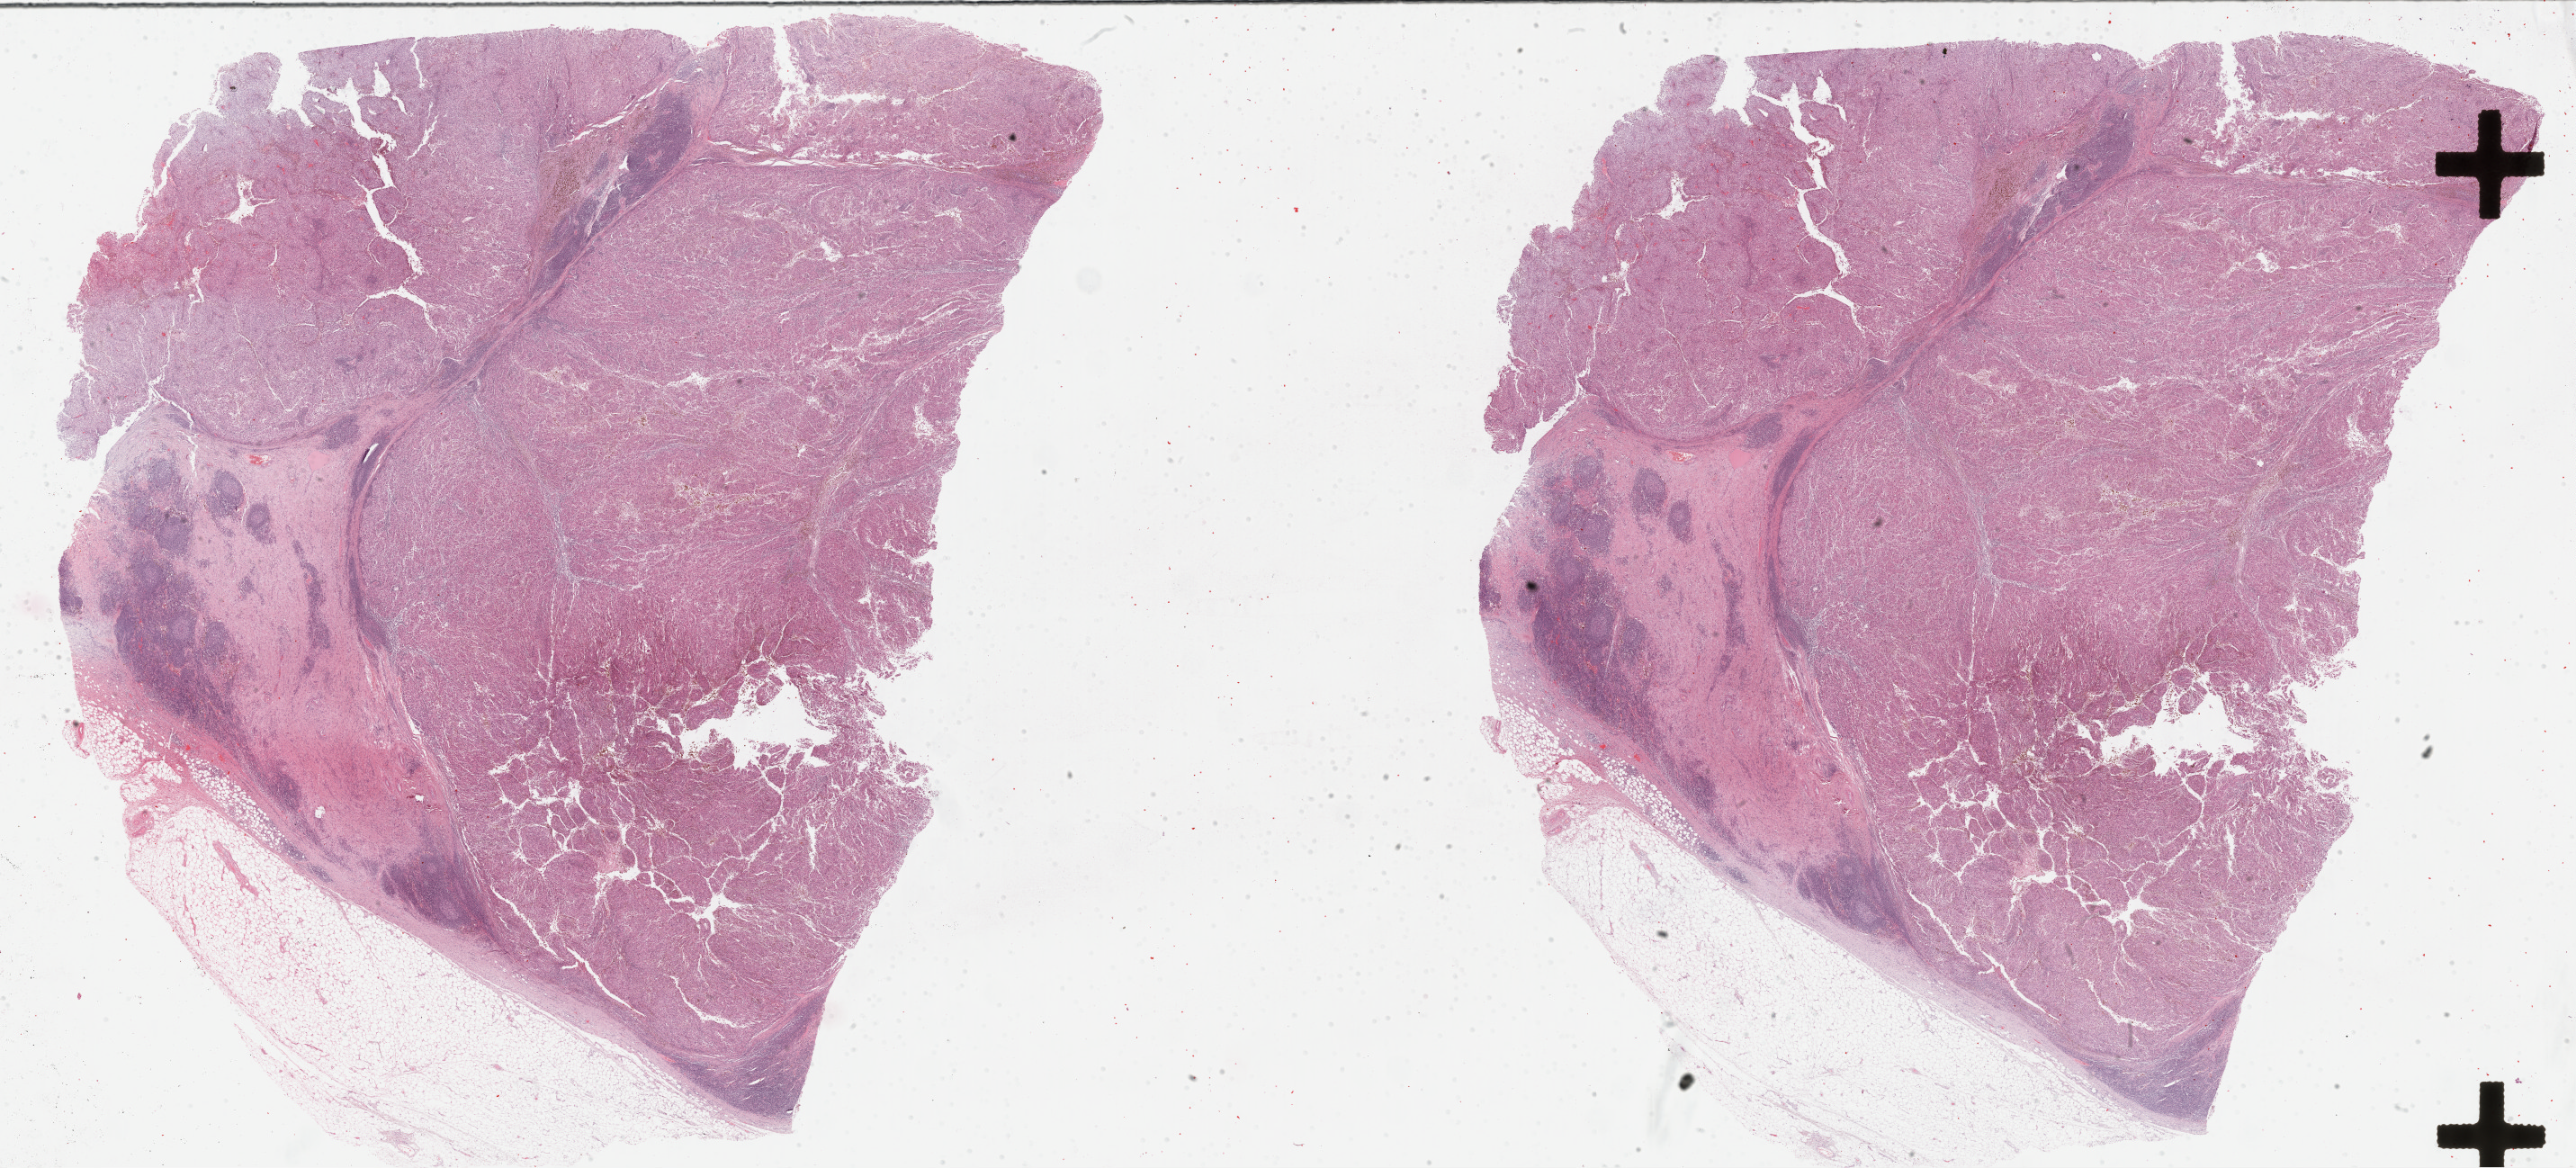
H&E-stained whole-slide image, shown as a low-resolution overview of the whole scanned area (about 46.3 x 21.0 mm), formalin-fixed paraffin-embedded (FFPE) diagnostic section, skin, primary tumour sample. Female, age 75 years at initial diagnosis.
- pathologic diagnosis: Malignant melanoma, NOS
- AJCC pathologic stage: IIIA (7th edition)